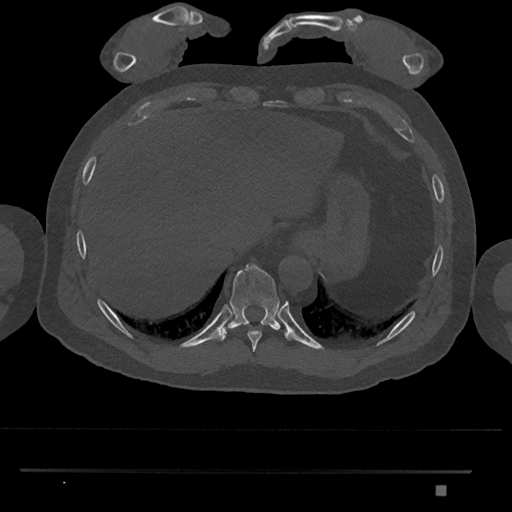
CT including the spine, one axial slice; position 1022 of 1134 along the scan axis; reconstruction kernel Br40s/3; bone window (W 1800 / L 400 HU); 0.5 mm slice thickness; 512 × 512 image matrix, field of view 429 × 429 mm. Male patient, age 65 years. Case-level facts recorded for this patient, not image findings: primary cancer: prostate.
Structures marked on this image (semi-automatically segmented with operator editing):
- T10 vertebra: bounding box [x1, y1, x2, y2] px = [220, 264, 281, 341]
- T9 vertebra: [237, 326, 262, 352]